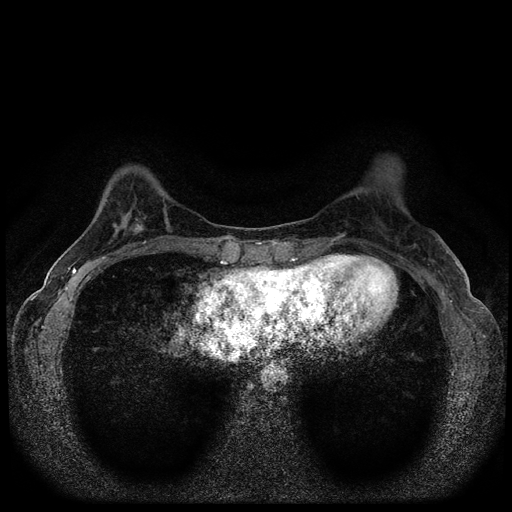
Breast MRI (dynamic contrast-enhanced, multi-phase), one axial slice; position 31 of 116 along the scan axis; dynamic contrast-enhanced series, time point 2 of 5 at this slice position (early post-contrast); 1.5 T; TE 2.7 ms, TR 5.6 ms; 2 mm slice thickness; 512 × 512 image matrix, field of view 310 × 310 mm. Female patient, age 40 years.
Annotated regions visible in this slice (semi-automatically segmented with operator editing):
- breast lesion (labelled benign in the annotation): box from (x=124, y=214) to (x=148, y=239) px